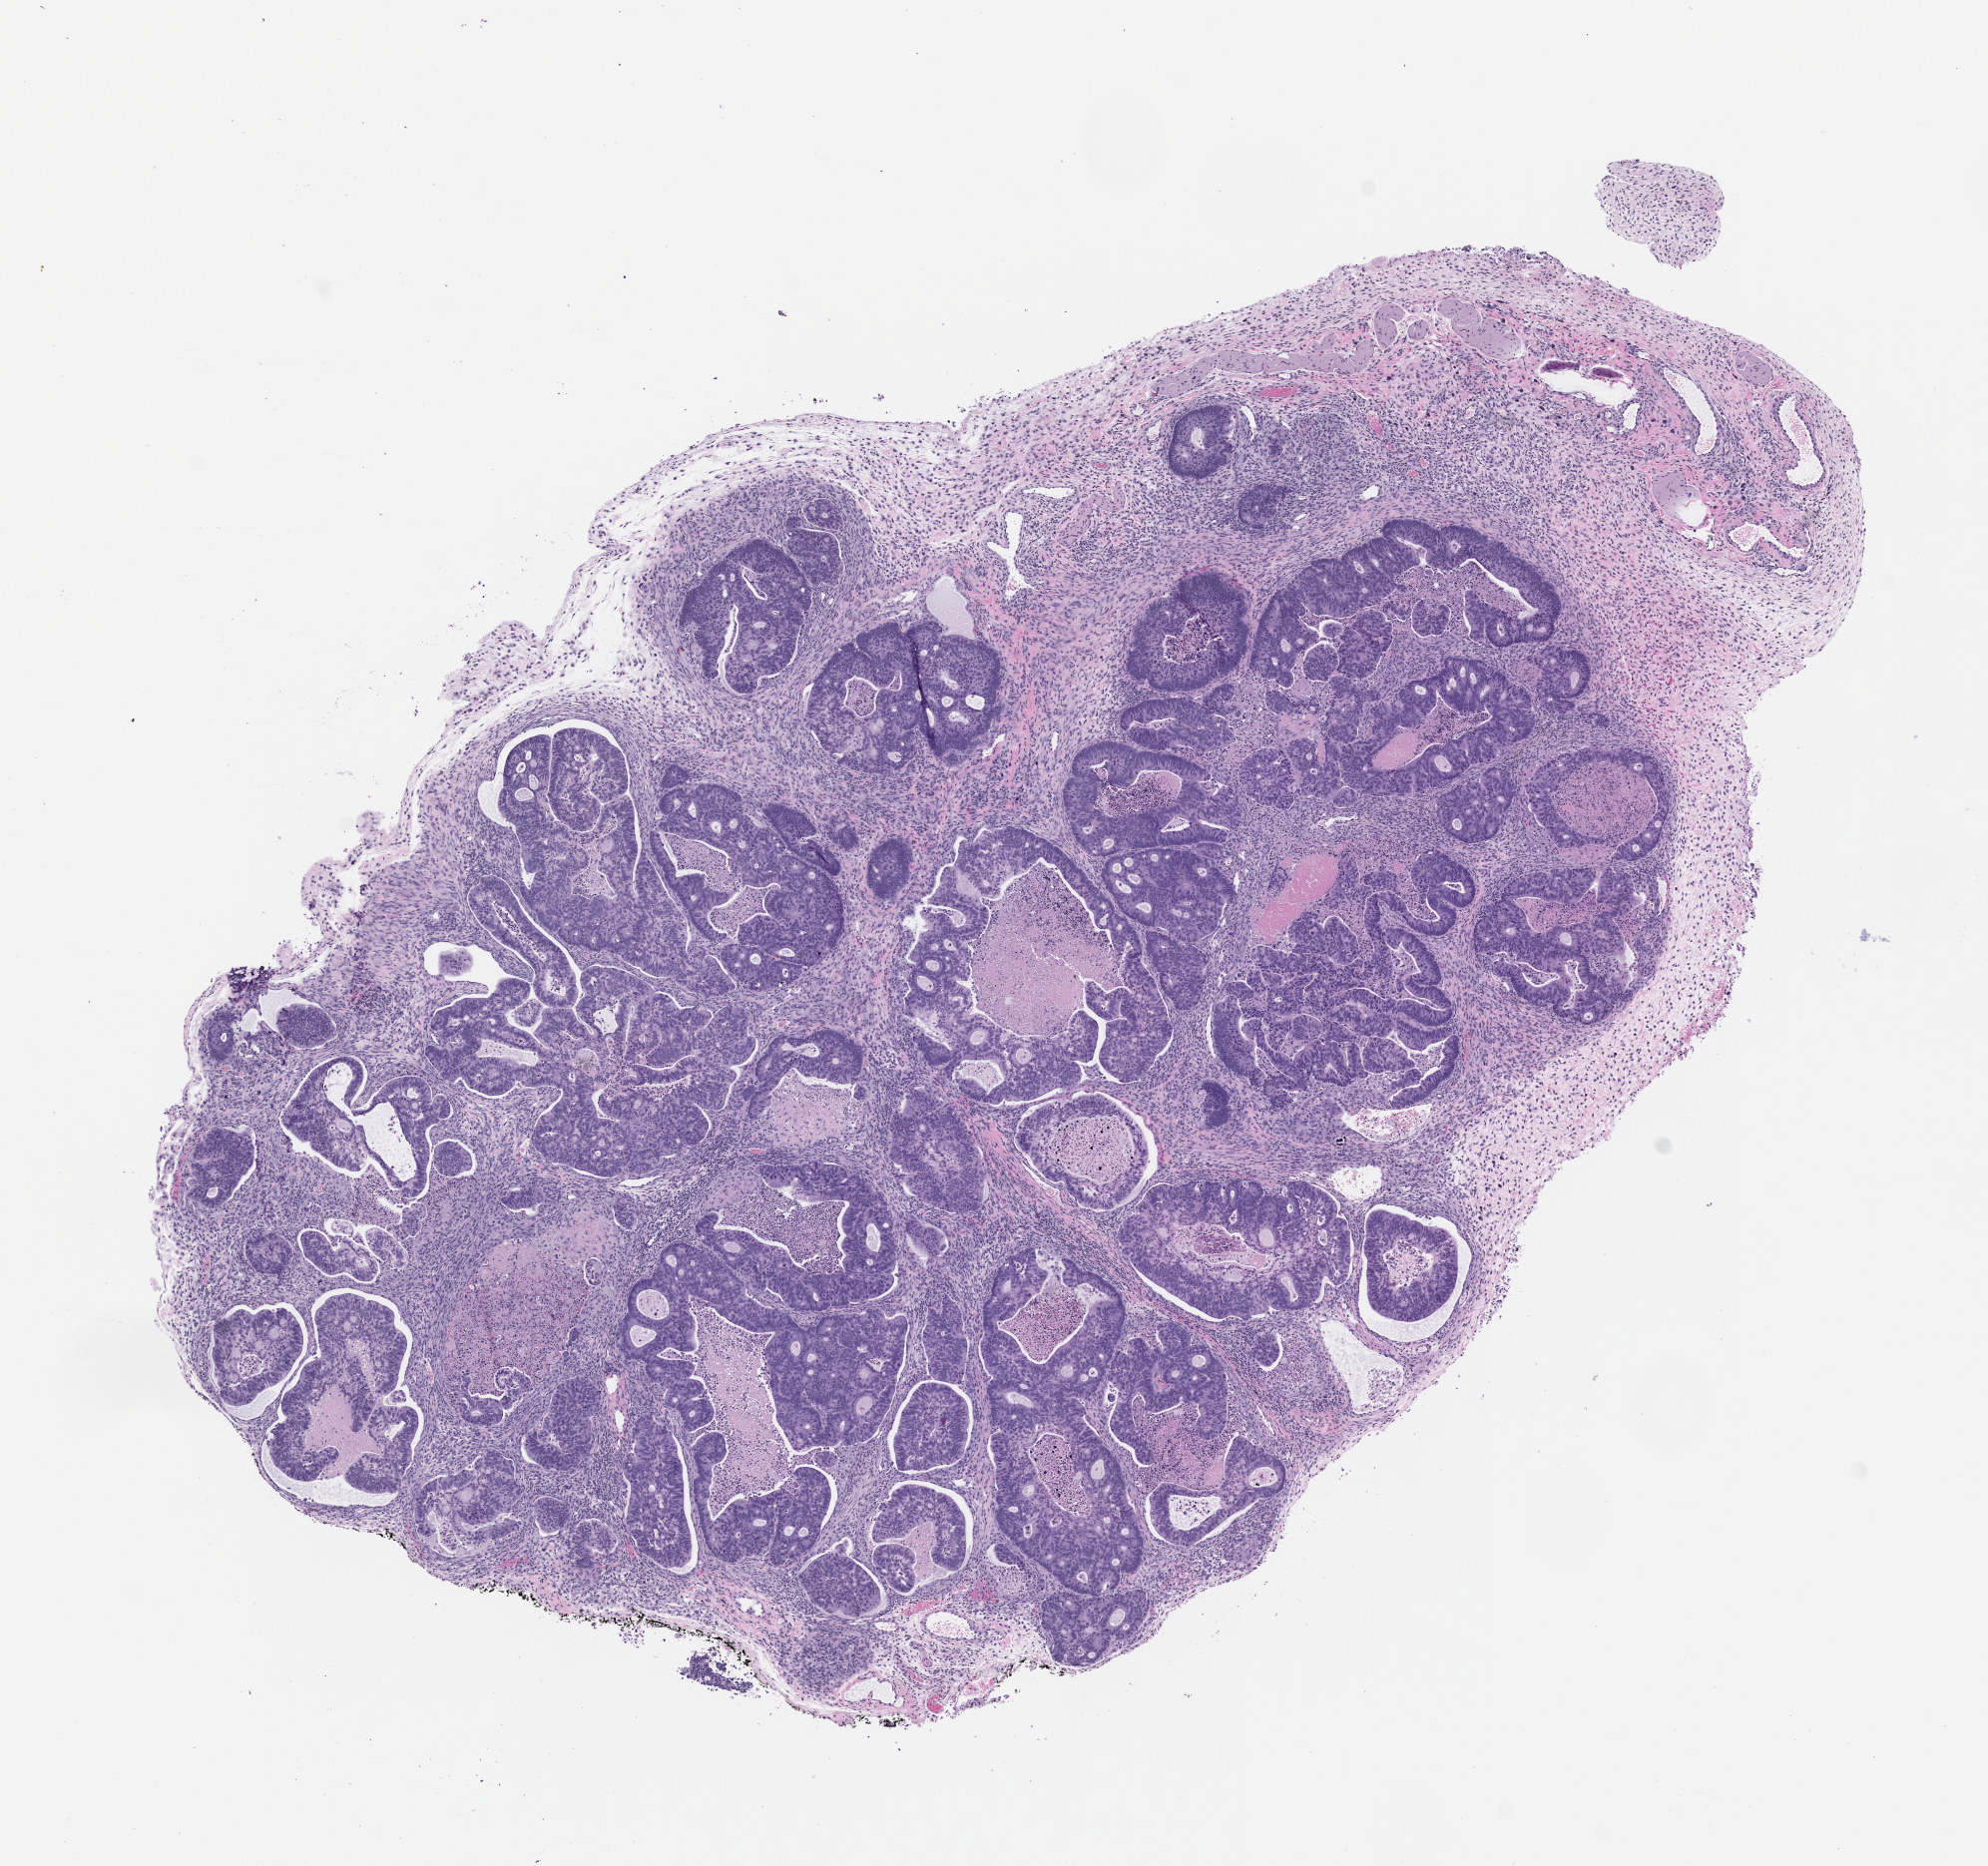
Whole-slide image, haematoxylin and eosin: patient-derived xenograft (human tumor grown in a mouse), passage 1 — whole scanned area (about 8.0 x 7.5 mm) shown as a low-resolution overview; formalin-fixed paraffin-embedded section; originating tumor site category: colon.
Originating patient diagnosis: Colon Adenocarcinoma.